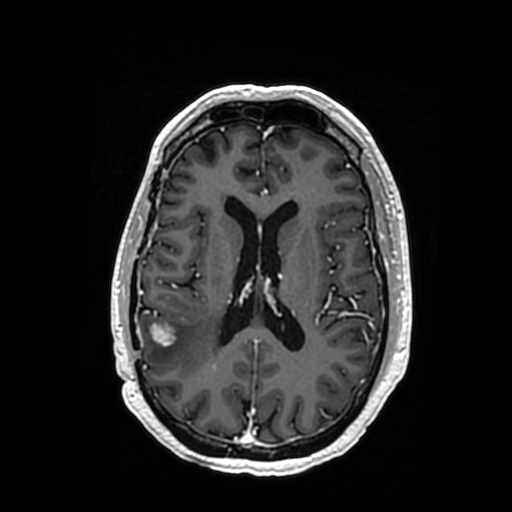
Brain MRI from a brain-tumour surgery series, one axial slice. Position 158 of 364 along the scan axis. T1-weighted post-contrast. 512 × 512 image matrix, field of view 260 × 260 mm. Case-level facts recorded for this patient, not image findings: histopathology: Oligodendroglioma; WHO grade: 3; IDH mutation: yes; tumour location: Right Posterior Temporal Inferior Parietal.
Outlined on this slice (manually delineated by an expert):
- tumour: box from (x=146, y=323) to (x=217, y=371) px